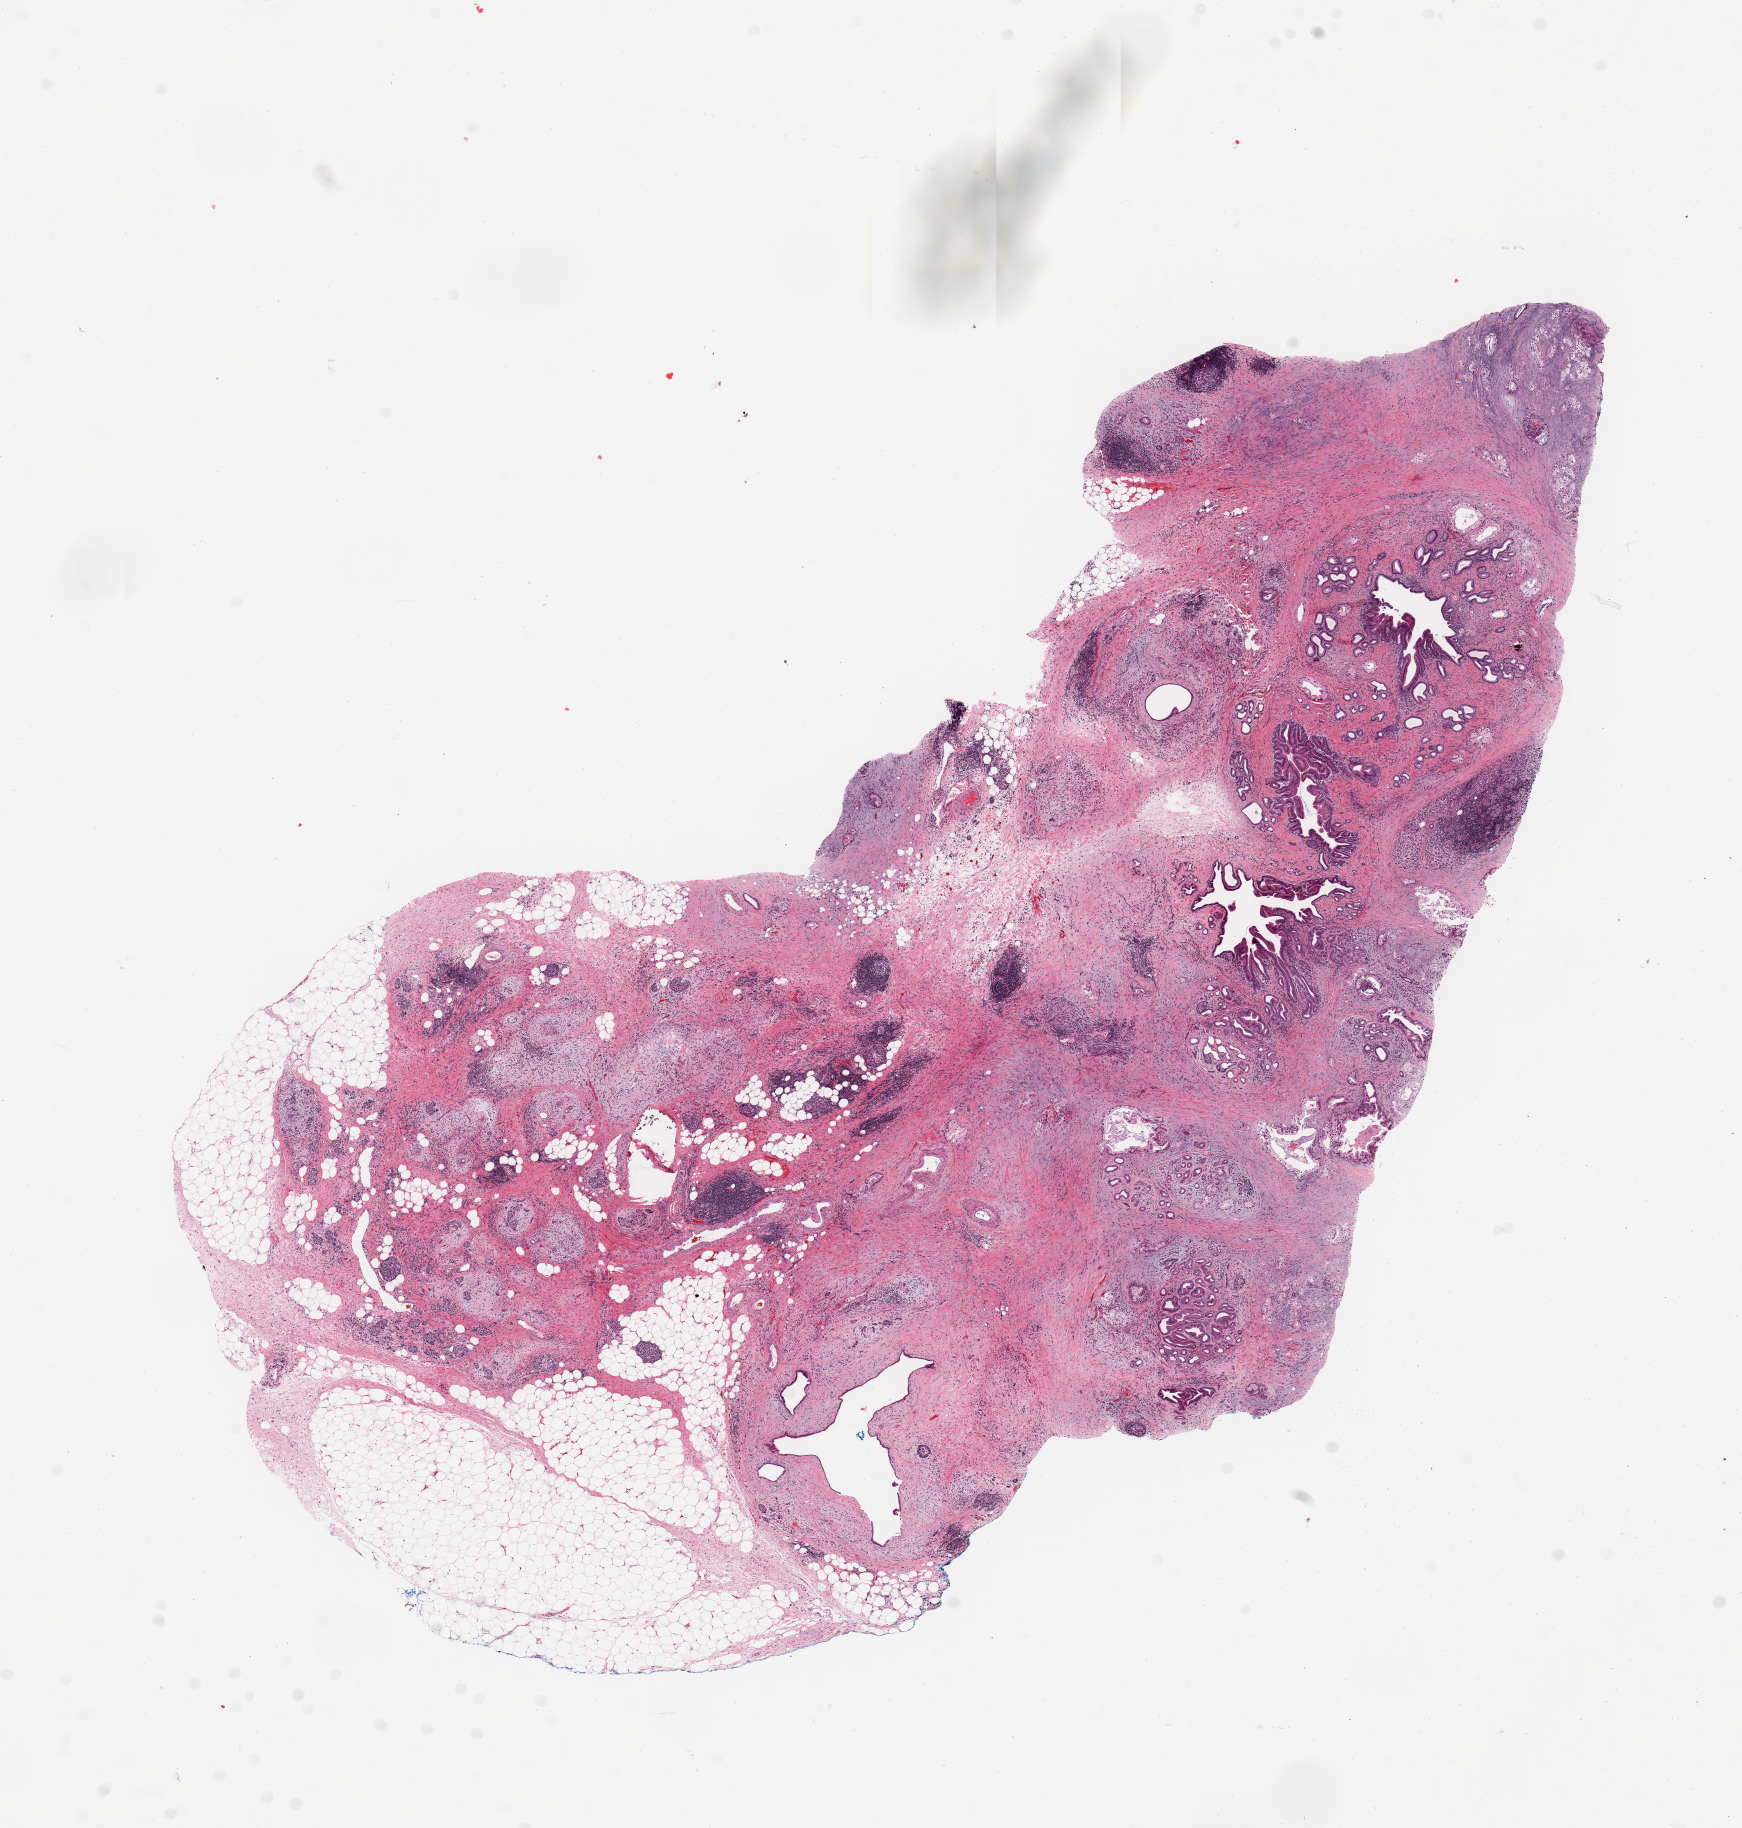
Digitized H&E tissue section (whole slide) — shown as a low-resolution overview of the whole scanned area (about 13.8 x 14.5 mm, acquisition: 20x scan). Pancreas, tumour tissue. Male, 42 y/o. Histologic grade: G3 (poorly differentiated).
* histologic diagnosis: Infiltrating duct carcinoma, NOS
* primary tumour site (as recorded): head
* AJCC pathologic stage: IIB